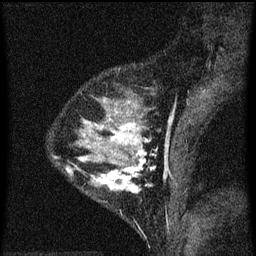
Breast MRI (dynamic contrast-enhanced), one sagittal slice; slice 21 of 60 in the series (ordered by position); dynamic contrast-enhanced series, image 2 of 3 at this slice position (ordered by acquisition); 1.5 T; TE 4.2 ms, TR 8 ms; 2 mm slice thickness; 256 × 256 image matrix. Female patient, age 33 years.
Annotated regions visible in this slice (semi-automatic segmentation, software-assisted and operator-edited):
- analysis volume of interest (the breast-tissue region the enhancement analysis was run in; not a lesion): bounding box <67,118,157,215> (left, top, right, bottom; pixels)
- tumour enhancement mask (voxels above the 70 % enhancement threshold inside the analysis volume of interest): <95,124,153,193>